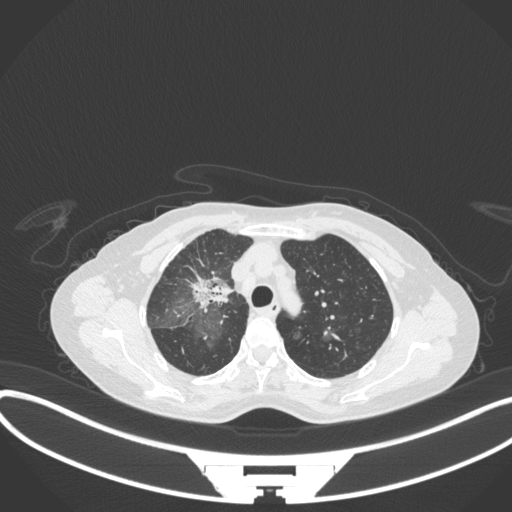
Chest CT, one axial slice; position 242 of 311 along the scan axis; reconstruction kernel B31f; 120 kVp; lung window (W 1500 / L -600 HU); 512 × 512 image matrix. Patient: female, 59 years. Case-level facts recorded for this patient, not image findings: clinical TNM (as recorded): T3 N0 M0.
Annotated regions visible in this slice (bounding box drawn by a radiologist):
- lung tumour (recorded histology: adenocarcinoma): box from (x=182, y=268) to (x=233, y=311) px